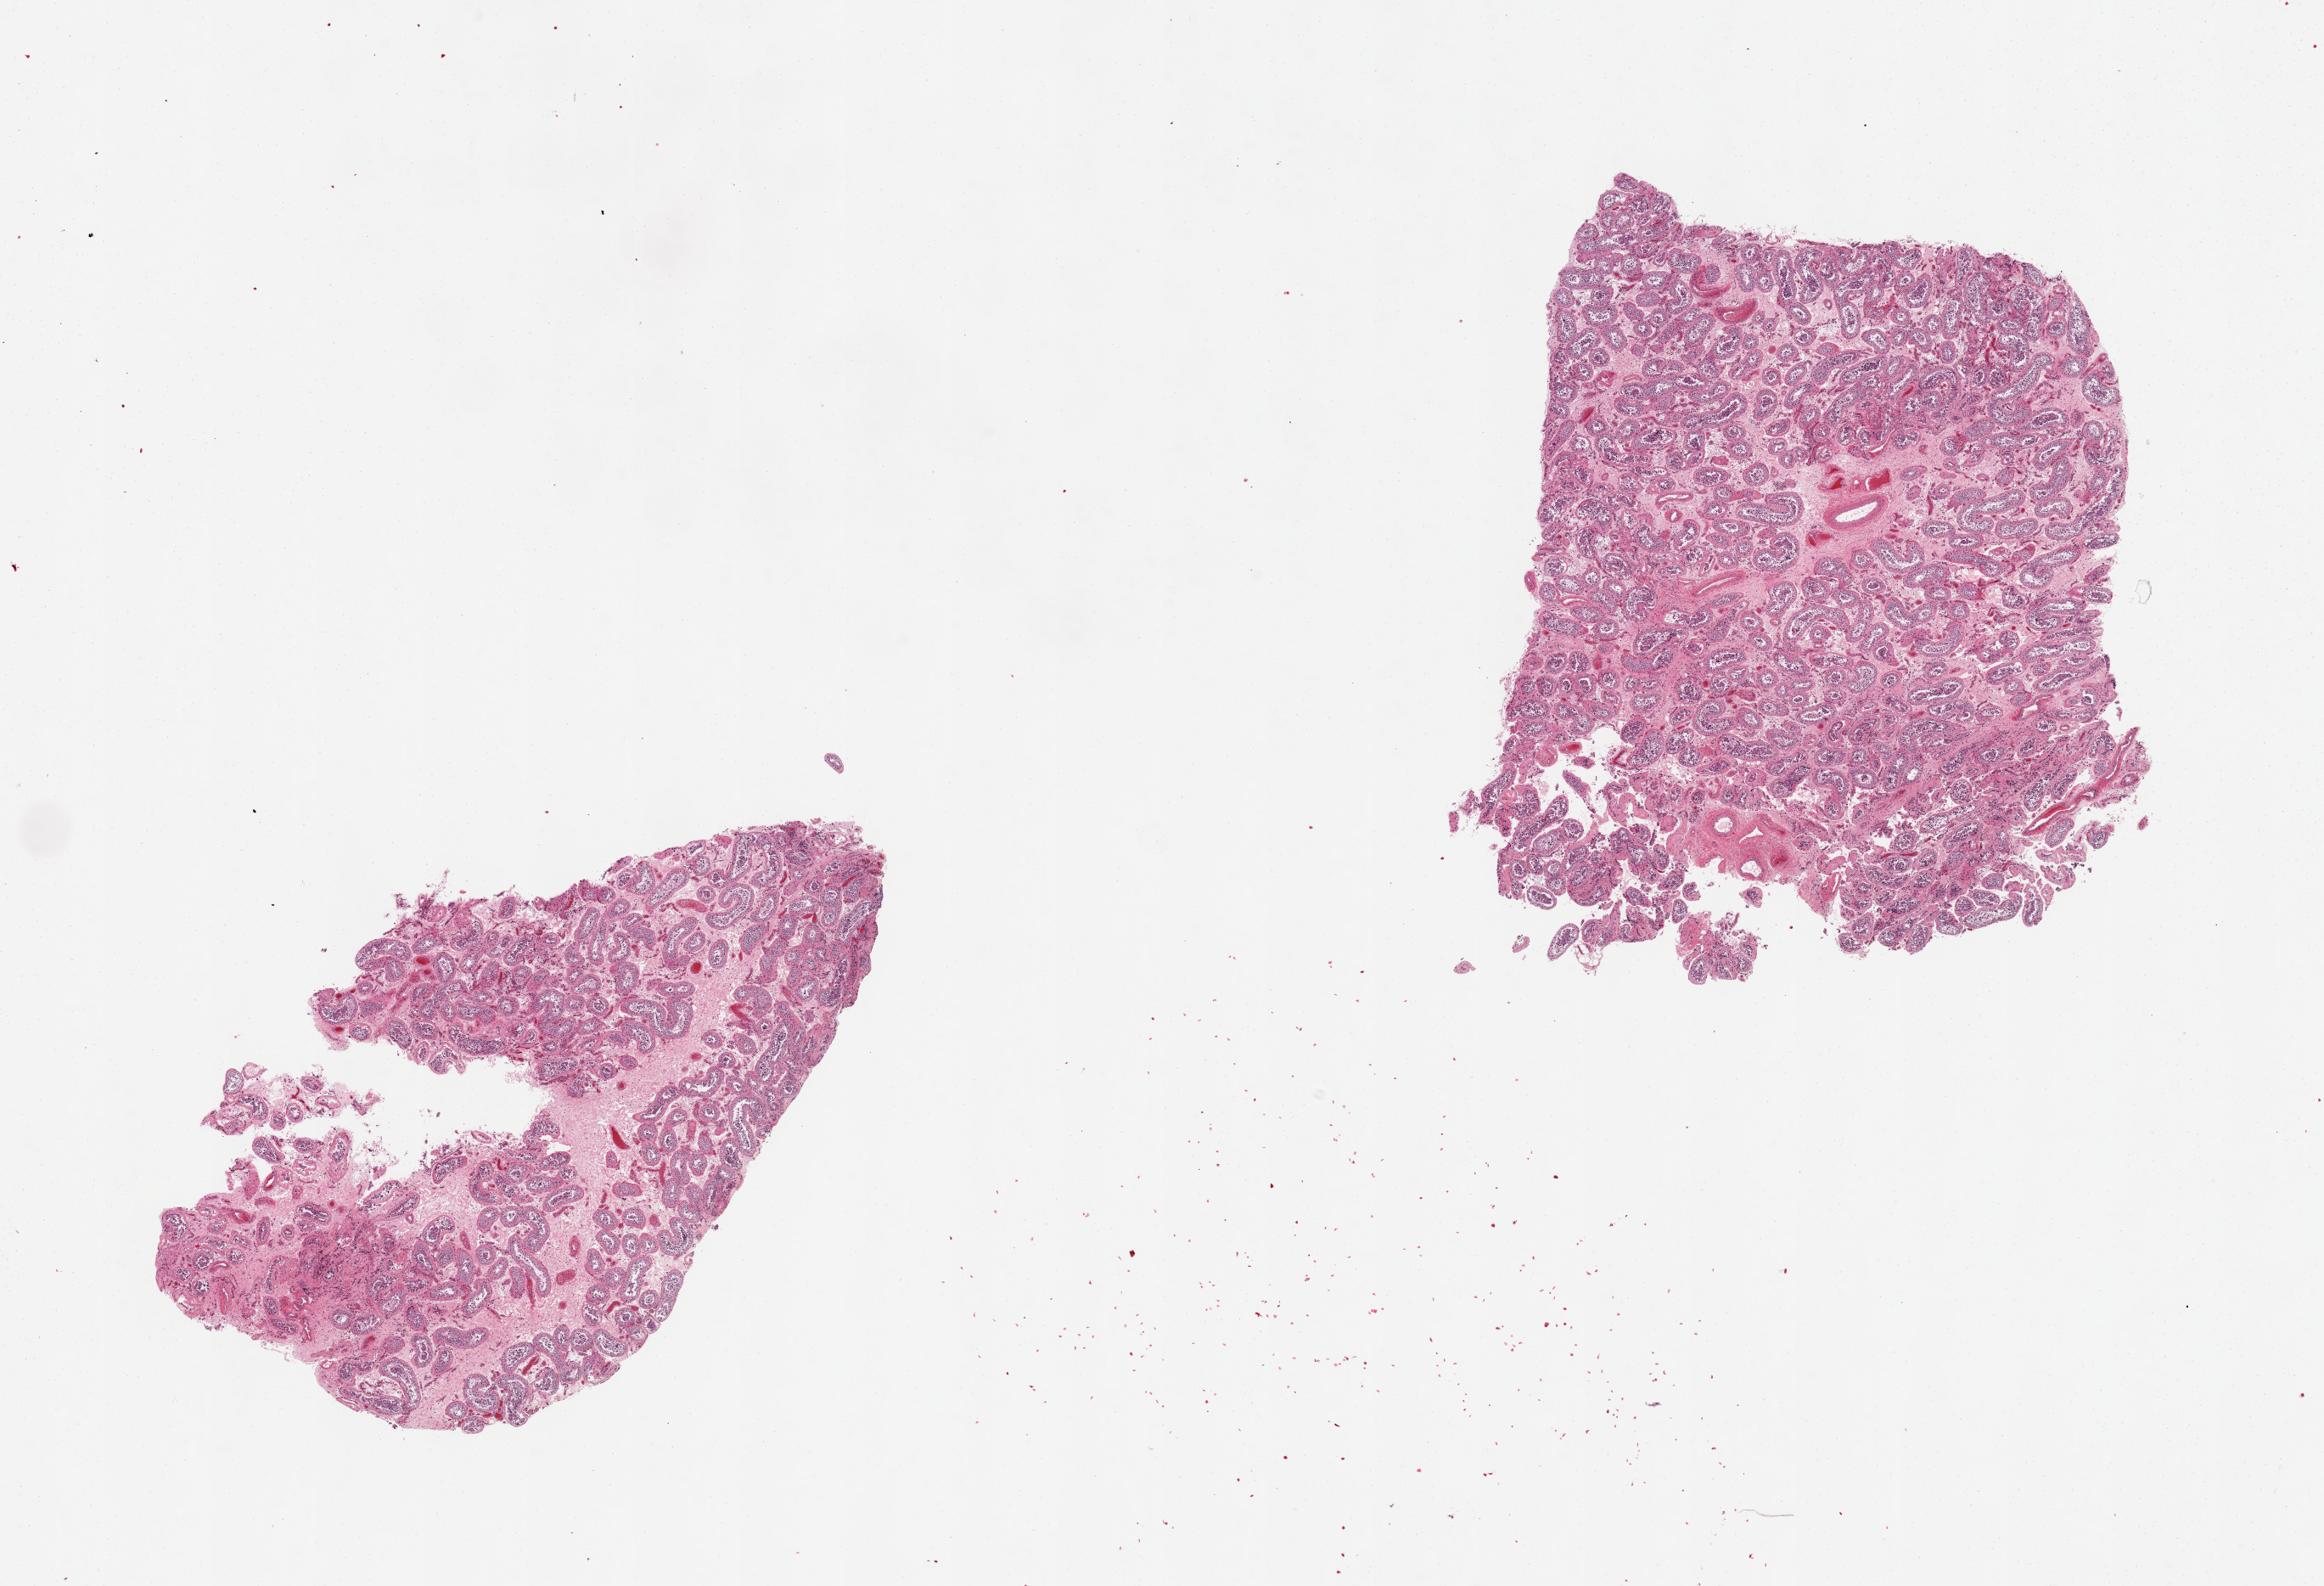
Digitized haematoxylin and eosin-stained section, shown as a low-resolution overview of the whole scanned area (about 21.7 x 14.8 mm), PAXgene-fixed paraffin-embedded (PFPE) section, sampled site (target tissue): testis, donor tissue sample.
Reviewer comment on this tissue sample: 2 pieces. Reduced spermatogenesis.